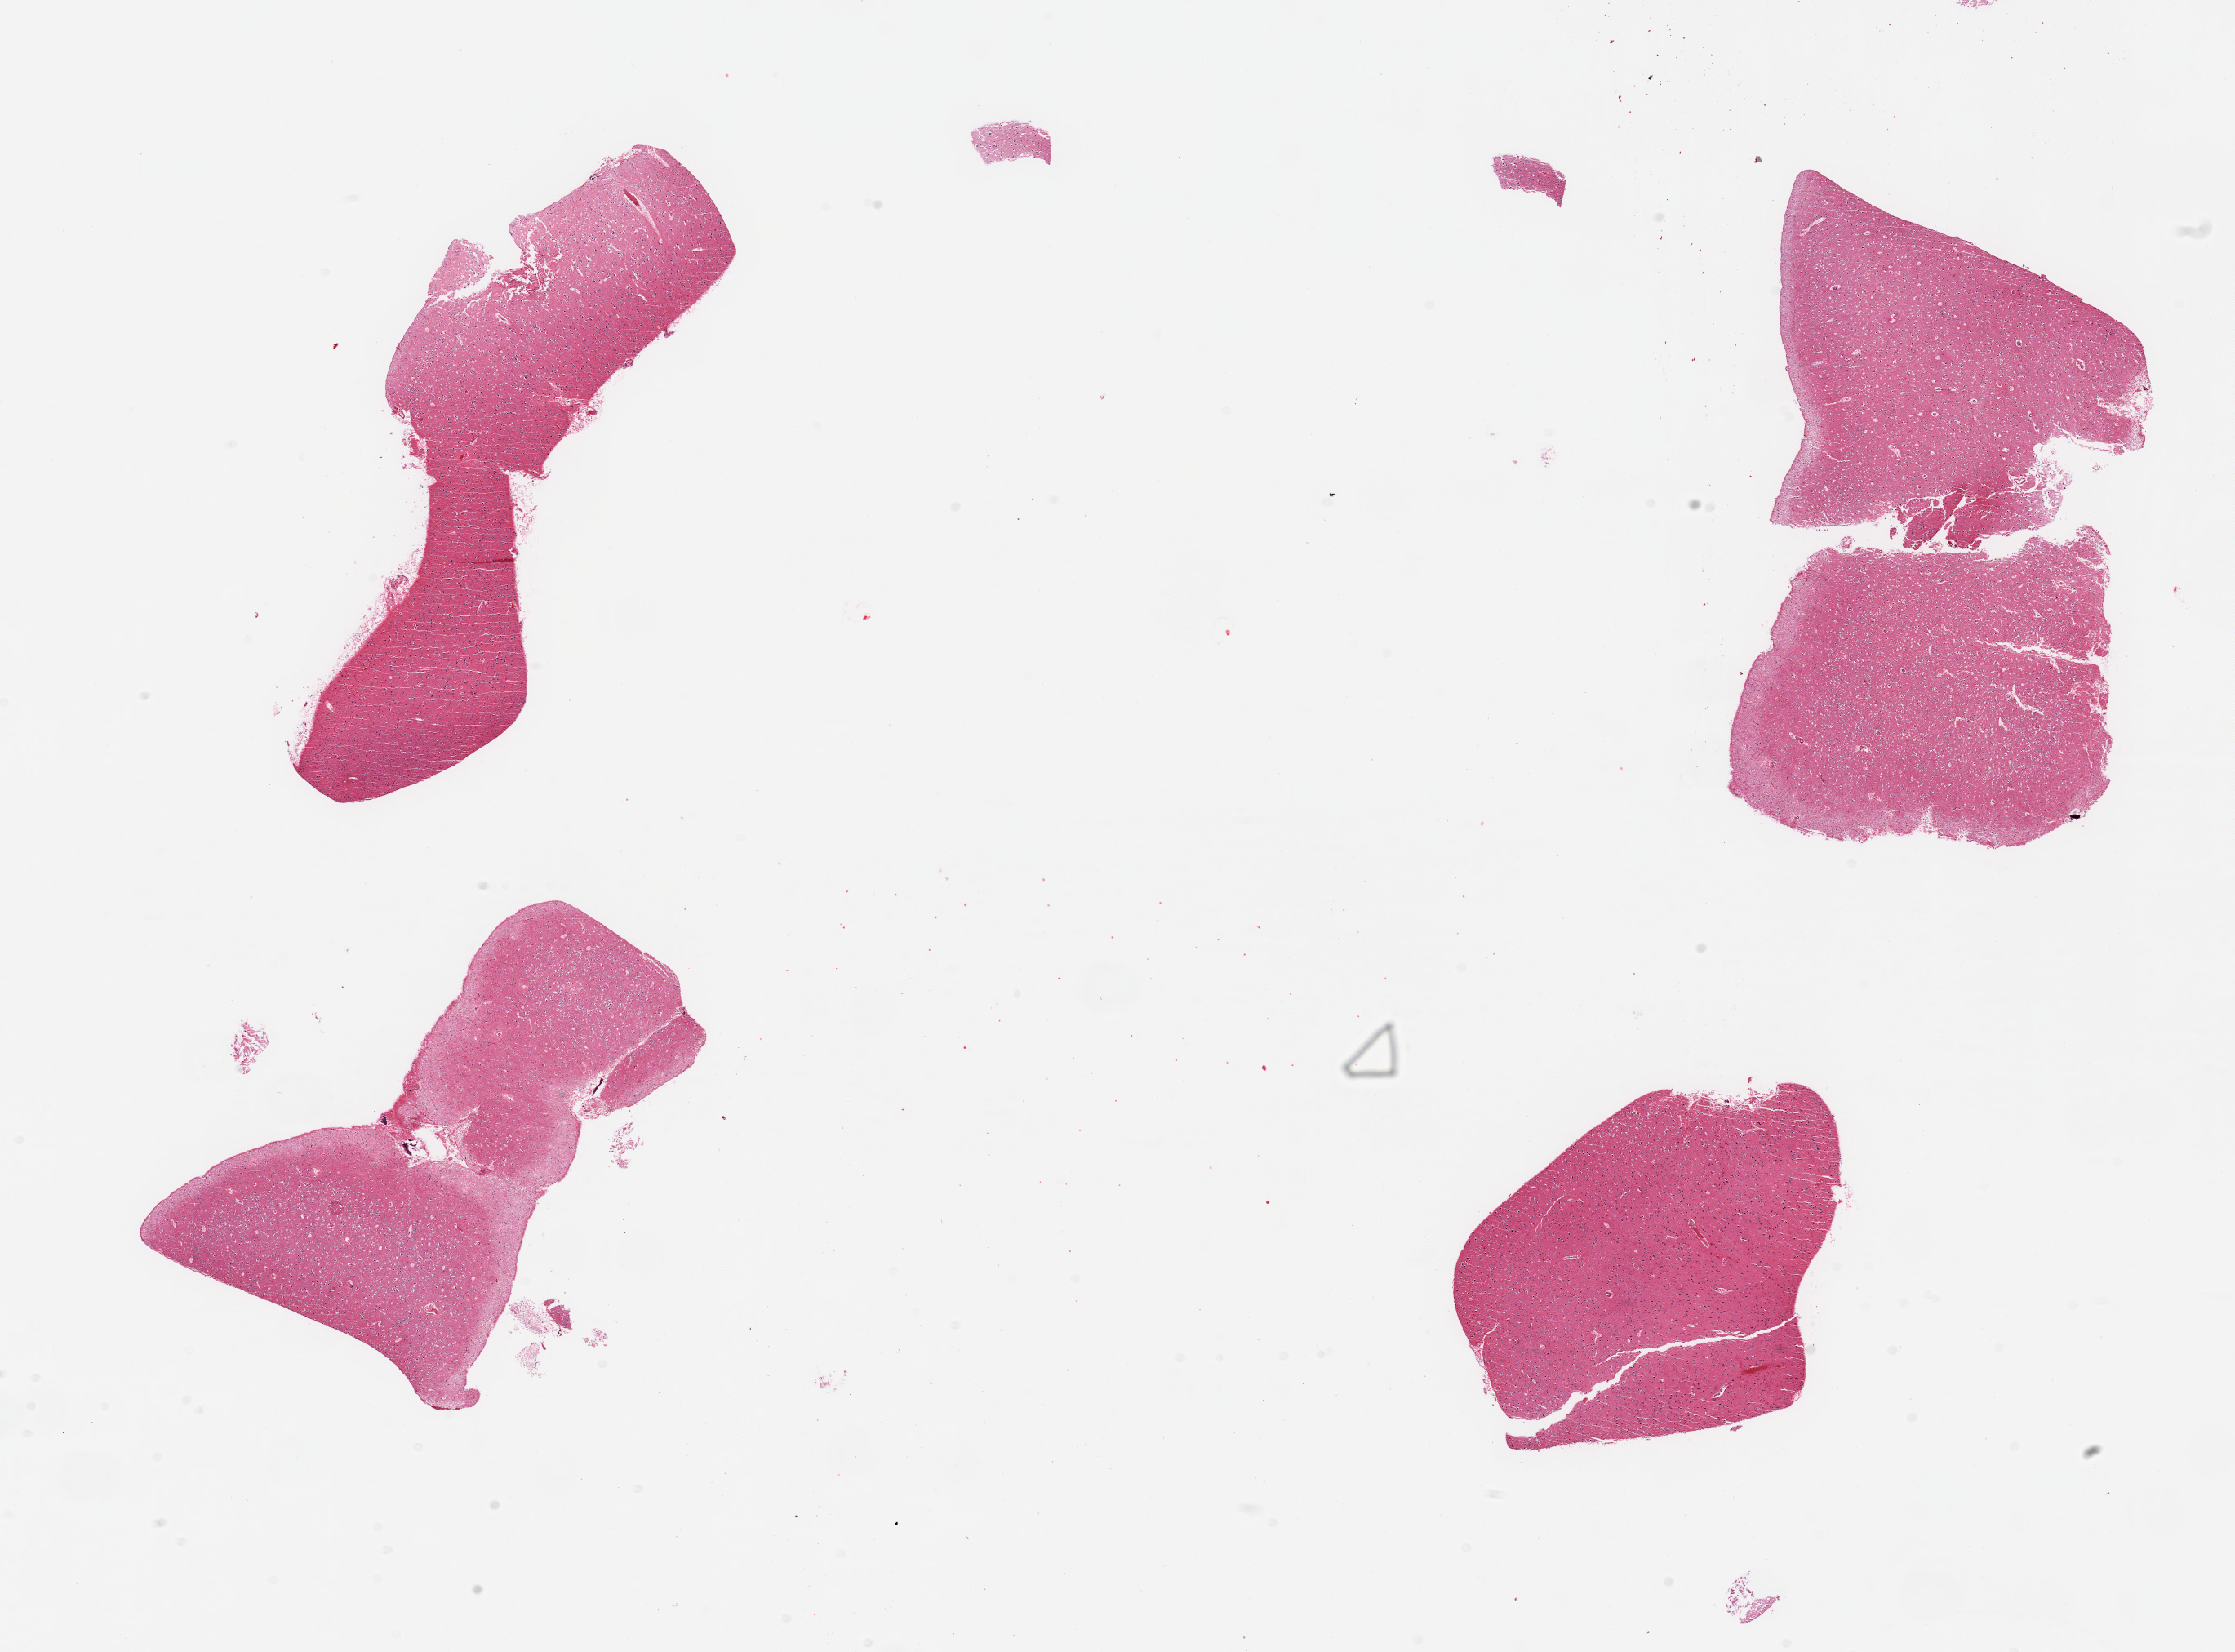
Whole-slide image, hematoxylin and eosin (H&E) stain, brightfield, low-resolution overview of the scanned area, about 21.7 x 16.0 mm. PAXgene-fixed paraffin-embedded (PFPE) section. Target tissue: cerebral cortex. Donor tissue sample. Male donor.
Pathologist's review note for this sample: 4 pieces, no abnormalities.